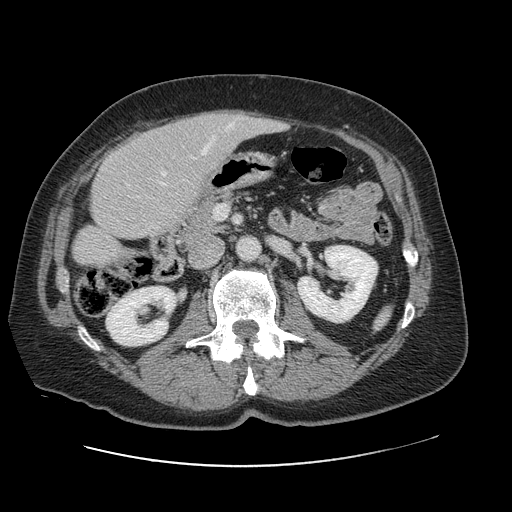
Contrast-enhanced abdominal CT, one axial slice. Position 36 of 138 along the scan axis. Intravenous contrast given. Soft-tissue window (W 400 / L 40 HU). 2.5 mm slice thickness. 512 × 512 image matrix. Male patient, age 71 years. Case-level facts recorded for this patient, not image findings: diagnosis: colorectal cancer liver metastases, imaged before liver resection; multiple liver metastases: no; largest metastasis: 3.3 cm; disease in both lobes: no.
Structures marked on this image (expert manual segmentation):
- hepatic veins: bounding box <162,124,233,184> (left, top, right, bottom; pixels)
- liver: <74,111,280,266>
- planned liver remnant (the part of the liver to remain after resection): <74,133,190,266>
- portal vein (with intrahepatic branches): <162,172,166,176>